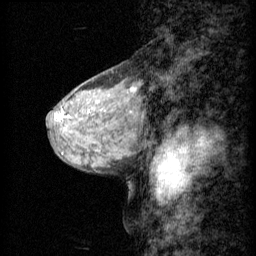
Breast MRI (dynamic contrast-enhanced), one sagittal slice. Slice 22 of 60 in the series (ordered by position). 3 images stored at this slice position (order not interpretable as contrast timing). 1.5 T. TE 4.2 ms, TR 11 ms. 1.5 mm slice thickness. 256 × 256 image matrix, field of view 200 × 200 mm. Female patient, age 48 years.
Annotated regions visible in this slice (semi-automatically segmented with operator editing):
- analysis volume of interest (the breast-tissue region the enhancement analysis was run in; not a lesion): box from (x=61, y=76) to (x=142, y=143) px
- tumour enhancement mask (voxels above the 70 % enhancement threshold inside the analysis volume of interest): (x=133, y=88)–(x=135, y=91)